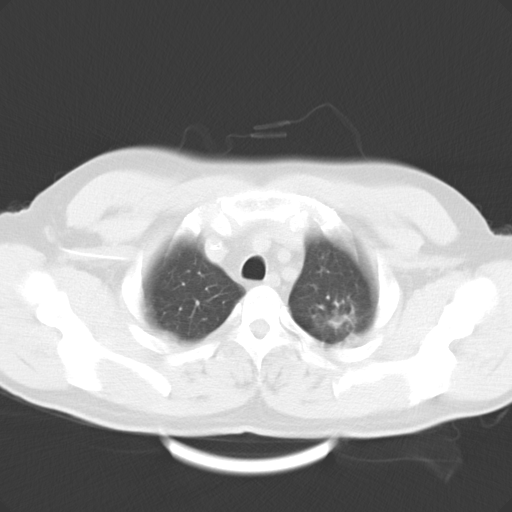
Chest CT, one axial slice. Slice 17 of 20 in the series (ordered by position). 120 kVp. Lung window (W 1500 / L -600 HU). 10 mm slice thickness. 512 × 512 image matrix, field of view 362 × 362 mm. Patient: male, 45 years. From the clinical record (not read from this slice): clinical TNM (as recorded): T2 N0 M0.
Annotated regions visible in this slice (bounding box drawn by a radiologist):
- lung tumour (recorded histology: adenocarcinoma): box from (x=304, y=289) to (x=365, y=348) px